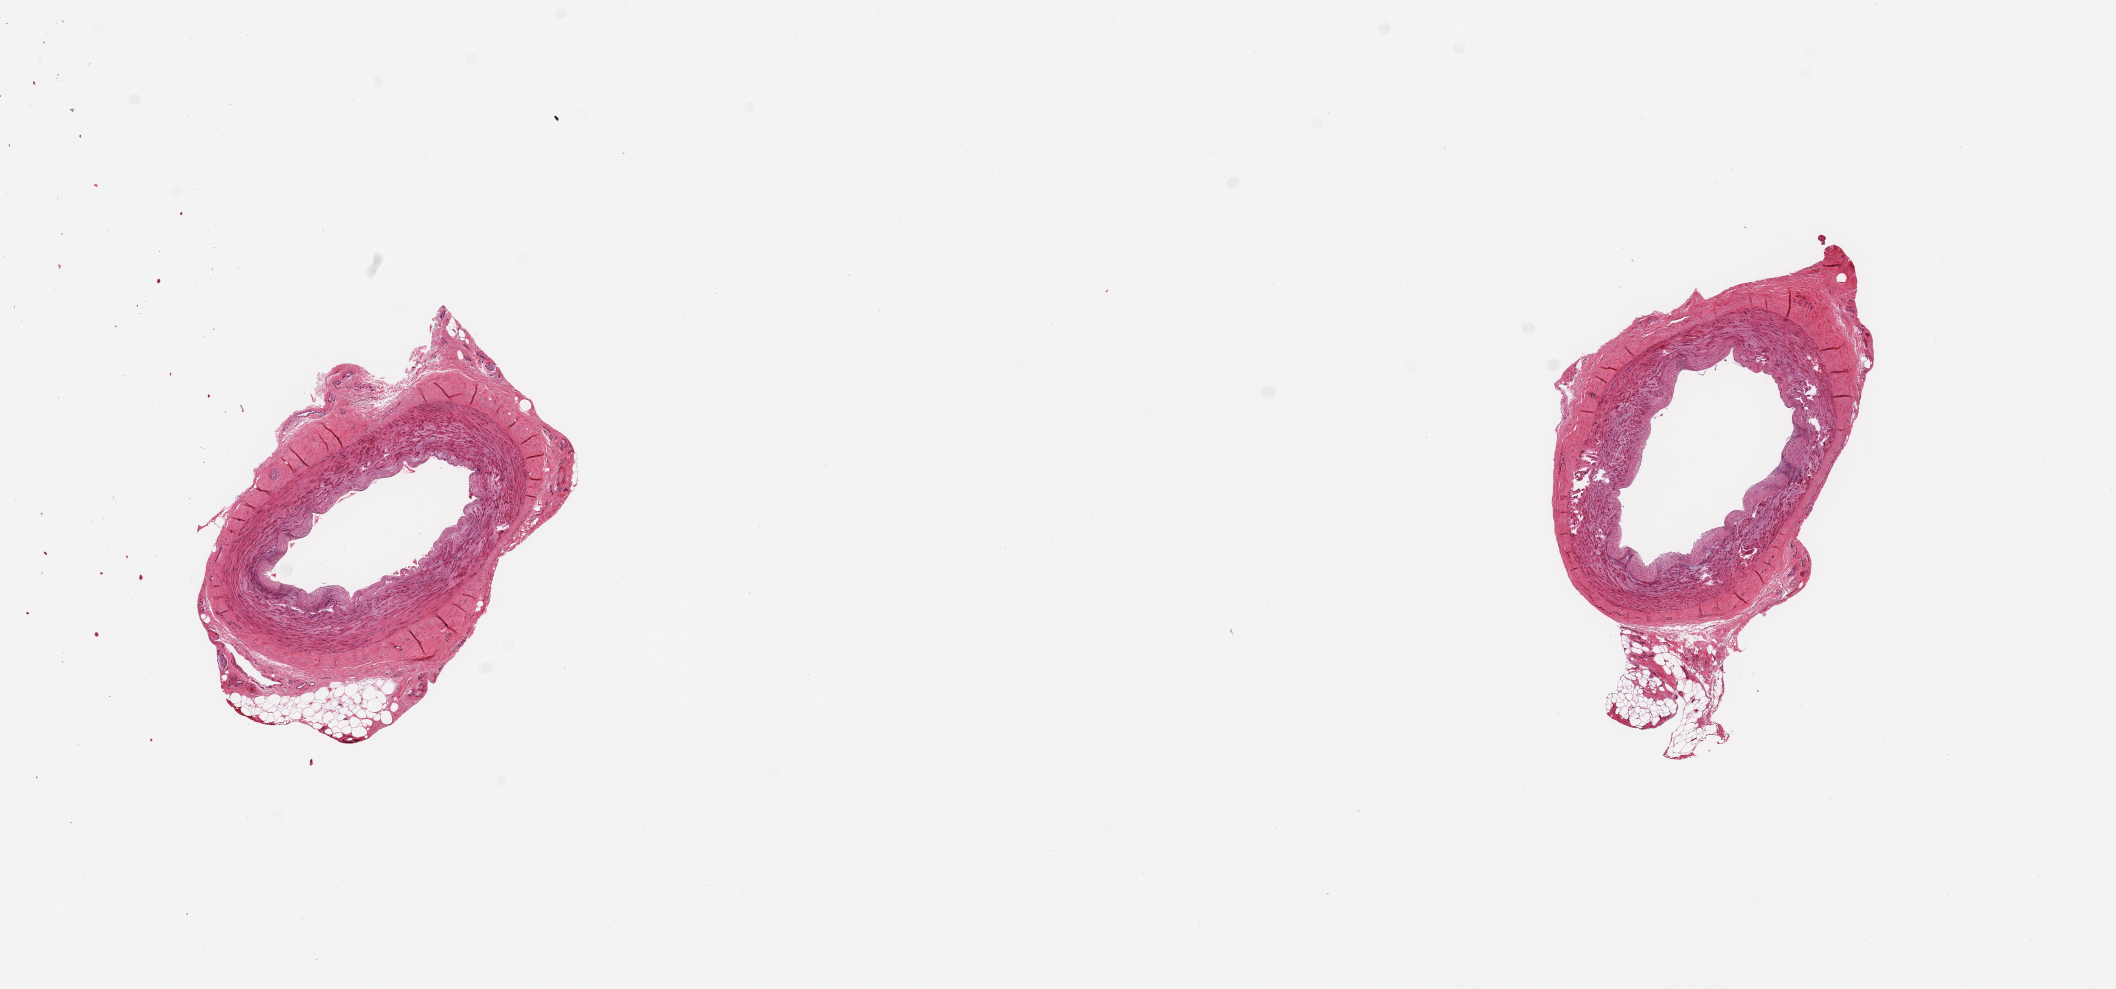
Whole-slide image, haematoxylin and eosin stain, brightfield, a low-resolution overview of the entire scanned area, about 16.7 x 7.8 mm (slide scanned at 20x); PAXgene-fixed, paraffin-embedded tissue; section of tibial artery (target tissue); tissue donor sample. Donor sex: male.
Reviewer comment on this tissue sample: 2 pieces; 10% external fat content.